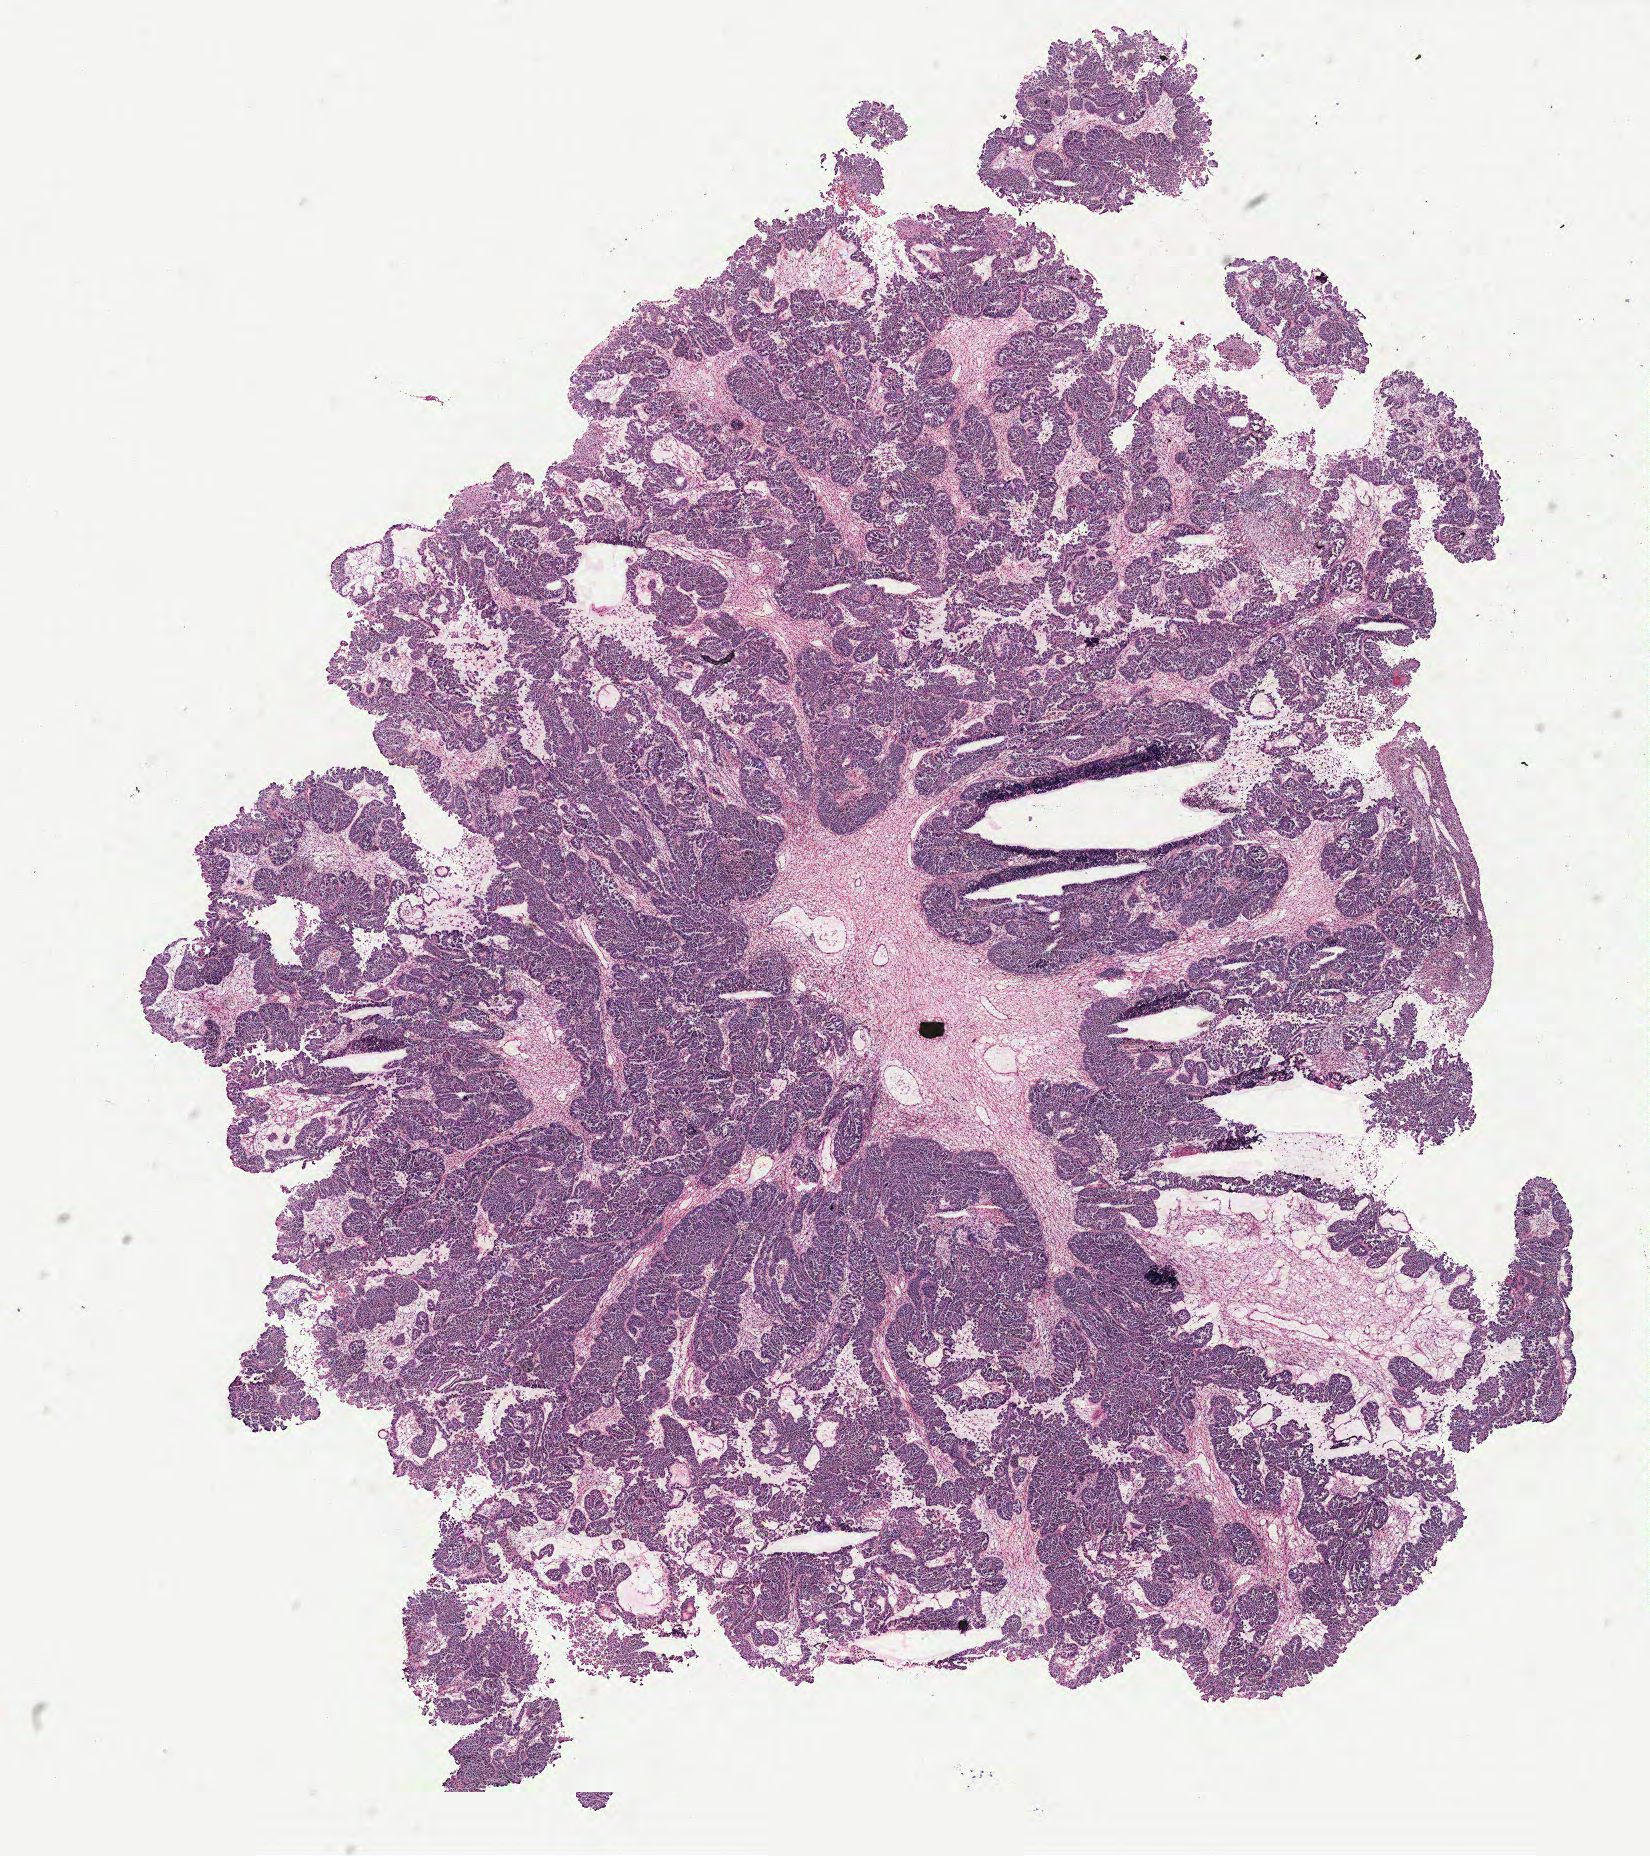
Digitized Hematoxylin and eosin (H&E) stained tissue section (whole slide), shown as a low-resolution overview of the whole scanned area (about 13.2 x 14.9 mm). Tumour tissue sample, ovary. Patient: female, age 48 years.
Histologic diagnosis: Serous adenocarcinoma, NOS (fallopian tube). Primary tumour site (as recorded): fallopian tube.